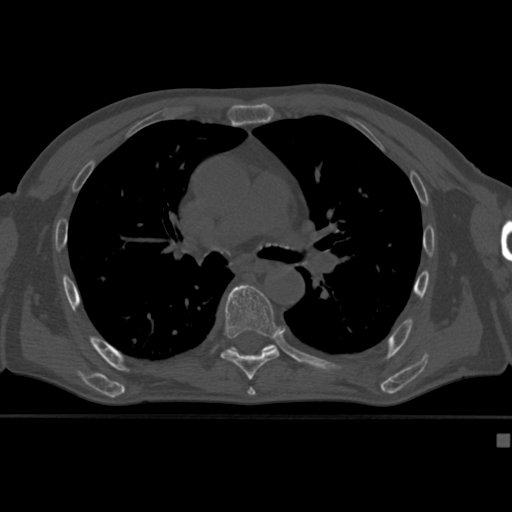
CT including the spine, one axial slice. Position 278 of 430 along the scan axis. Bone window (W 1800 / L 400 HU). 512 × 512 image matrix, field of view 337 × 337 mm. Patient: male, 64 years. From the clinical record (not read from this slice): primary cancer: uterus; vertebrae with lytic lesions (as recorded): T1, T4, T5, T7, L5.
Structures marked on this image (semi-automatic segmentation, software-assisted and operator-edited):
- T7 vertebra: bounding box [x1, y1, x2, y2] px = [221, 284, 280, 382]
- T8 vertebra: [264, 345, 276, 351]